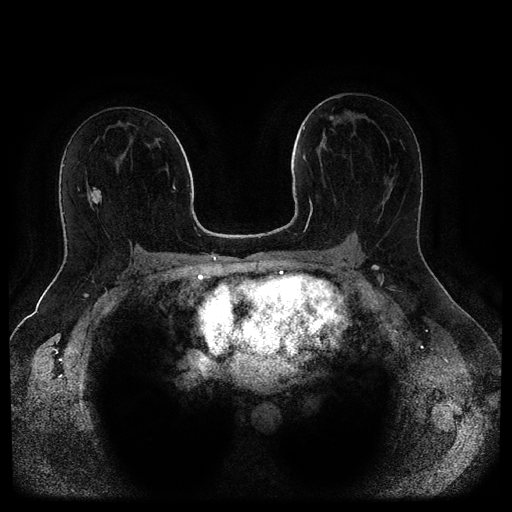
Breast MRI (dynamic contrast-enhanced, multi-phase), one axial slice. Slice 54 of 116 in the series (ordered by position). Dynamic contrast-enhanced series, time point 2 of 5 at this slice position (early post-contrast). 1.5 T. TE 2.6 ms, TR 5.3 ms. 2 mm slice thickness. 512 × 512 image matrix, field of view 370 × 370 mm. Female patient, age 44 years.
Structures marked on this image (semi-automatically segmented with operator editing):
- breast lesion (labelled benign in the annotation): box from (x=89, y=187) to (x=102, y=204) px